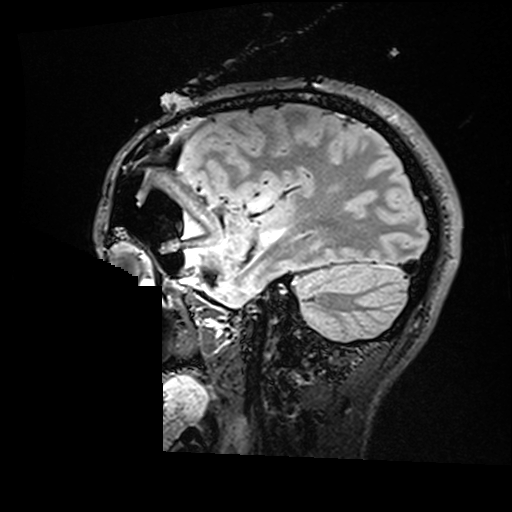
Brain MRI from a brain-tumour surgery series, one sagittal slice; slice 122 of 176 in the series (ordered by position); T2 FLAIR; 1 mm slice thickness; 512 × 512 image matrix. From the clinical record (not read from this slice): histopathology: Astrocytoma; WHO grade: 2; IDH mutation: yes; tumour location: Right Insular.
Outlined on this slice (expert manual segmentation):
- residual tumour: bounding box [x1, y1, x2, y2] px = [256, 189, 274, 208]